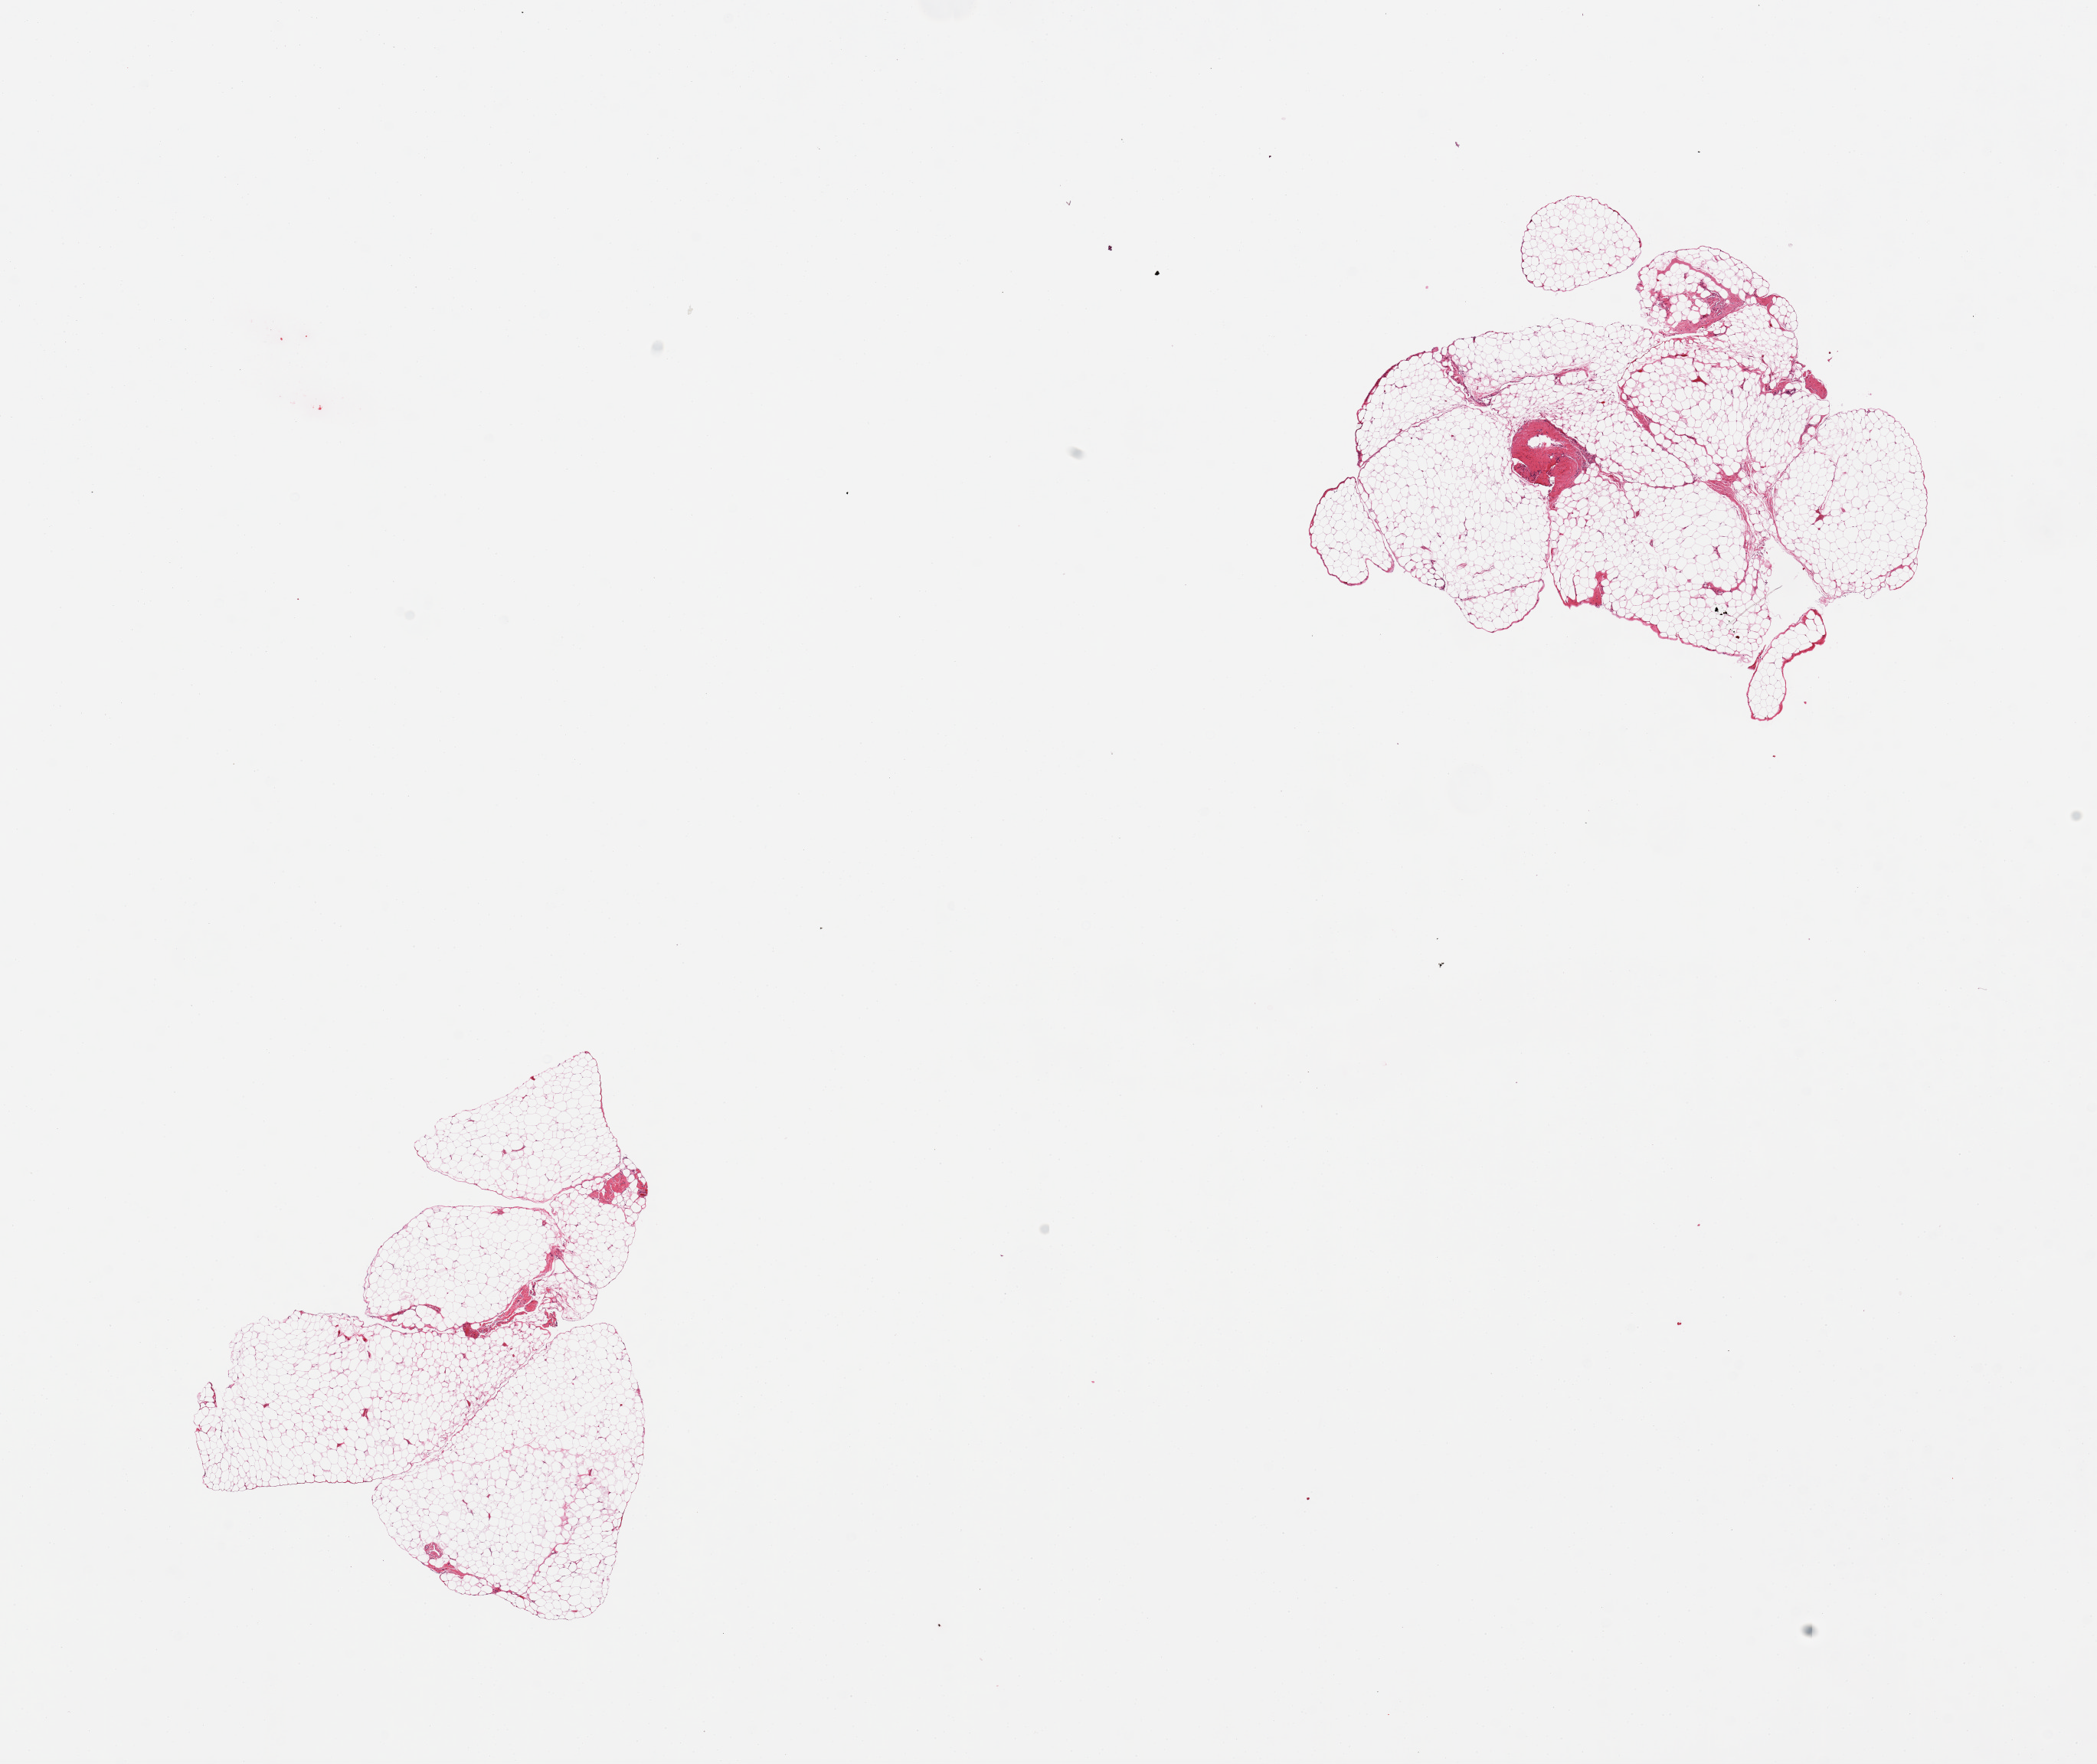
Digitized hematoxylin and eosin (H&E)-stained section, low-resolution overview of the scanned area, about 21.7 x 18.2 mm, PAXgene-fixed, paraffin-embedded tissue, sampled site (target tissue): omentum, donor tissue sample. Donor sex: male.
Pathologist's review note for this sample: 2 pieces.